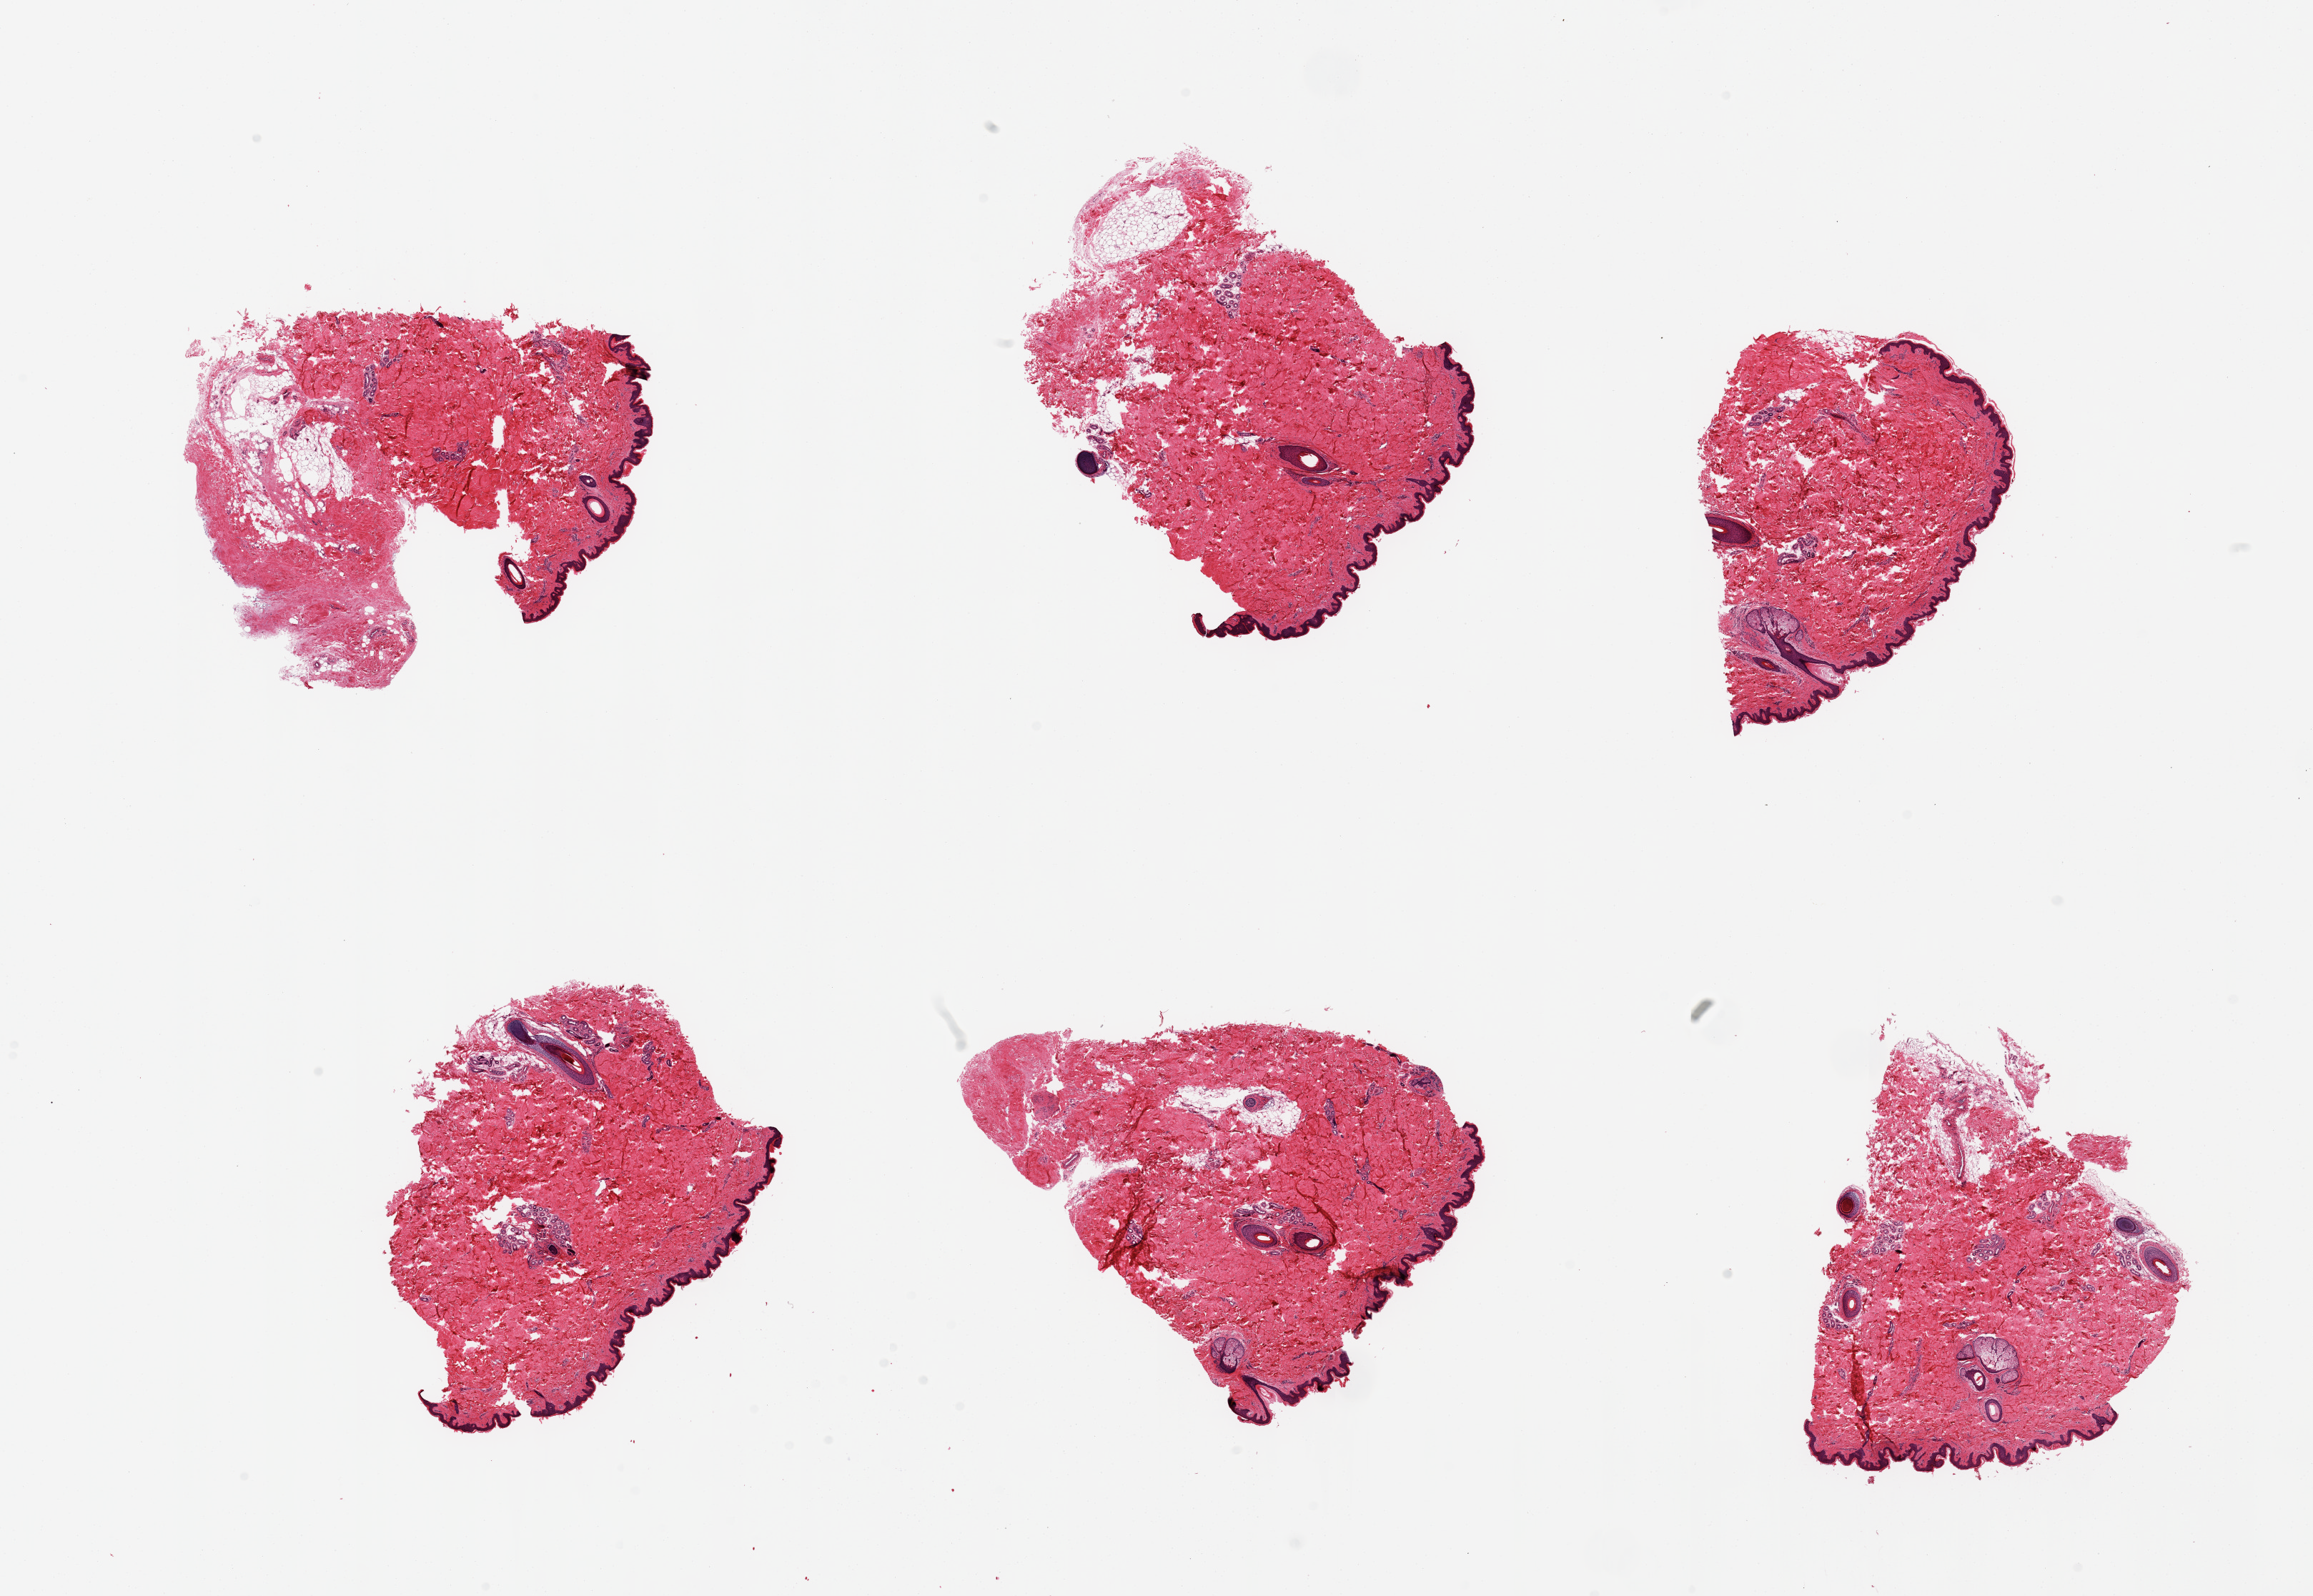
Digitized hematoxylin and eosin (H&E)-stained section, brightfield, whole scanned area (about 25.6 x 17.7 mm) shown as a low-resolution overview, PAXgene-fixed, paraffin-embedded tissue, section of skin of suprapubic region (target tissue), donor tissue sample.
* pathologist's review note for this sample: 6 pieces, trace dermal fat; squamous epithelium is ~50 microns